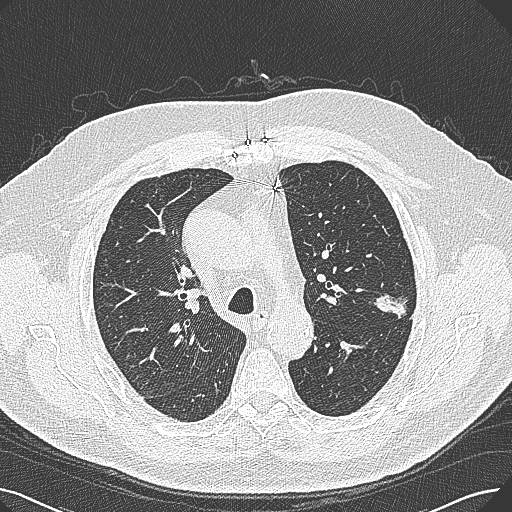
Low-dose screening chest CT, axial slice; first (baseline) screen; lung window (W 1500 / L -600 HU). Male, age 74 years at enrolment. Former smoker at enrolment.
Expert-annotated lung lesion, bounding box (x1, y1, x2, y2) in pixels: (367, 273, 427, 324). Reader record for this screening exam (exam-level; its link to the box is not recorded): non-calcified nodule or mass ≥4 mm, left upper lobe, 15 × 10 mm, poorly defined margins, soft tissue attenuation. Lung cancer was diagnosed 124 days after this screen: adenocarcinoma, NOS, left upper lobe, well differentiated (G1), stage IA (AJCC 6th edition), 26 mm at pathology.